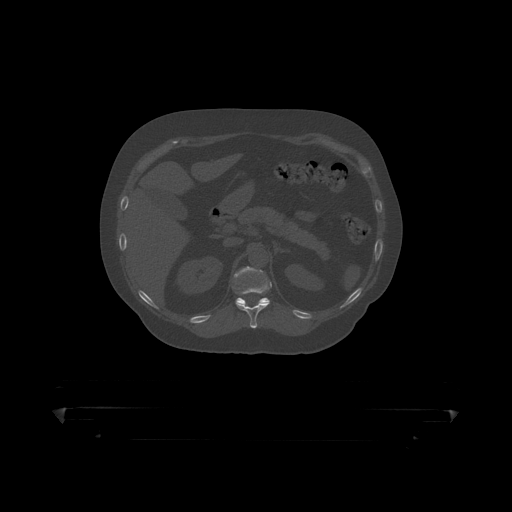
CT including the spine, one axial slice. Slice 185 of 390 in the series (ordered by position). Reconstruction kernel STANDARD. 120 kVp. Bone window (W 1800 / L 400 HU). 512 × 512 image matrix. Patient: male, 60 years. From the clinical record (not read from this slice): primary cancer: prostate.
Annotated regions visible in this slice (semi-automatic segmentation, software-assisted and operator-edited):
- T11 vertebra: box from (x=236, y=274) to (x=272, y=319) px
- T12 vertebra: (x=234, y=267)–(x=270, y=305)